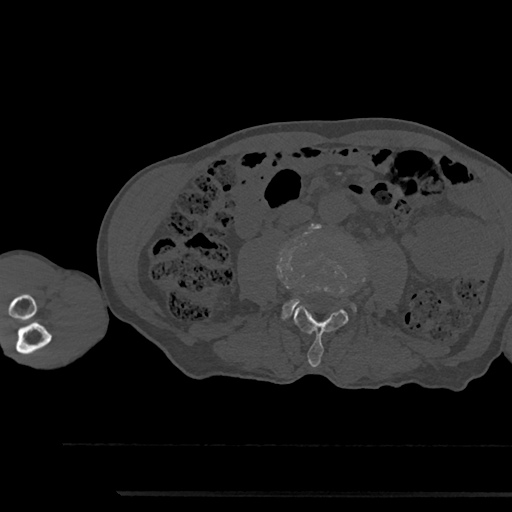
CT including the spine, one axial slice. Slice 456 of 797 in the series (ordered by position). 120 kVp. Bone window (W 1800 / L 400 HU). 0.5 mm slice thickness. 512 × 512 image matrix, field of view 367 × 367 mm. Male patient, age 79 years. From the clinical record (not read from this slice): primary cancer: prostate.
Outlined on this slice (semi-automatic segmentation, software-assisted and operator-edited):
- L3 vertebra: bounding box <294,306,349,367> (left, top, right, bottom; pixels)
- L4 vertebra: <283,287,356,317>